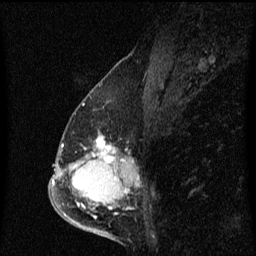
Breast MRI (dynamic contrast-enhanced), one sagittal slice; position 30 of 60 along the scan axis; dynamic contrast-enhanced series, image 2 of 3 at this slice position (ordered by acquisition); 1.5 T; TE 4.2 ms, TR 8.4 ms; 2 mm slice thickness; 256 × 256 image matrix, field of view 200 × 200 mm. Female patient, age 57 years. From the clinical record (not read from this slice): setting: breast cancer imaged before/during neoadjuvant chemotherapy; receptor status: HR-positive, HER2-negative.
Structures marked on this image (semi-automatic segmentation, software-assisted and operator-edited):
- analysis volume of interest (the breast-tissue region the enhancement analysis was run in; not a lesion): bounding box <66,132,129,177> (left, top, right, bottom; pixels)
- tumour enhancement mask (voxels above the 70 % enhancement threshold inside the analysis volume of interest): <96,138,116,173>